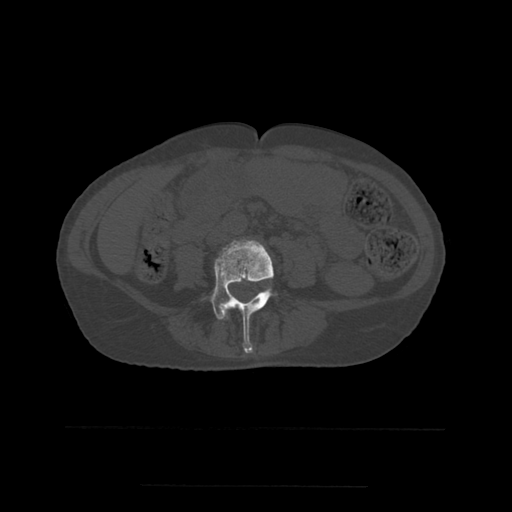
CT including the spine, one axial slice; position 168 of 544 along the scan axis; bone window (W 1800 / L 400 HU); 1.25 mm slice thickness; 512 × 512 image matrix. Patient age 58 years. From the clinical record (not read from this slice): primary cancer: lung.
Outlined on this slice (semi-automatic segmentation, software-assisted and operator-edited):
- L3 vertebra: bounding box [x1, y1, x2, y2] px = [254, 309, 260, 312]
- L4 vertebra: [204, 239, 278, 354]